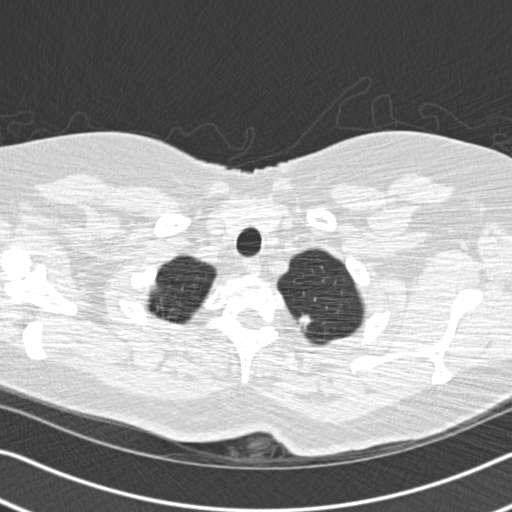
Axial slice from a low-dose chest CT screening exam. Baseline screening round. Lung window (W 1500 / L -600 HU). 1.25 mm slice thickness. 512 × 512 image matrix. Female, age 60 years at enrolment. Former smoker at enrolment.
- Lesion marked by an expert reader, bounding box (x1, y1, x2, y2) in pixels: (282, 305, 325, 343).
- Screening reader's record for this exam: no non-calcified nodule ≥4 mm recorded.
- Lung cancer was diagnosed 799 days after this screen (after the third annual screen): non-small cell carcinoma, left upper lobe, poorly differentiated (G3), stage IB (AJCC 6th edition), 16 mm at pathology.